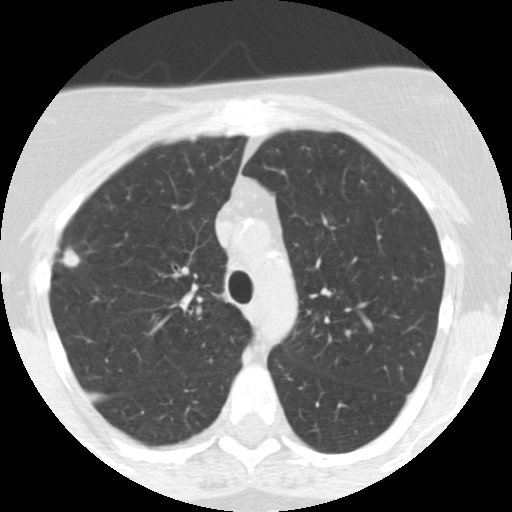
Chest CT (low-dose screening protocol), one axial image. Third annual screen. Lung window (W 1500 / L -600 HU). 2.5 mm slice thickness. Female, age 55 years at enrolment. Current smoker at enrolment.
Expert-annotated lung lesion, bounding box (x1, y1, x2, y2) in pixels: (47, 241, 91, 281). Screening reader's record for this exam (one nodule recorded; not confirmed to be the boxed lesion): non-calcified nodule or mass ≥4 mm, right upper lobe, 10 × 10 mm, poorly defined margins, soft tissue attenuation, pre-existing on the prior screen: yes; interval growth: yes. Official screen result: positive, other.